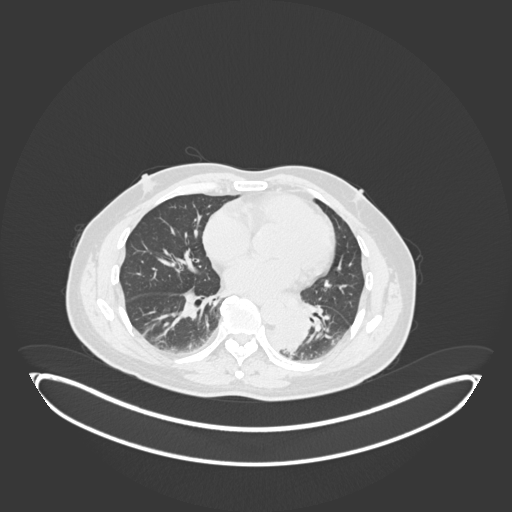
Chest CT, one axial slice; position 79 of 258 along the scan axis; lung window (W 1500 / L -600 HU); 512 × 512 image matrix, field of view 500 × 500 mm. Patient: male, 54 years. Case-level facts recorded for this patient, not image findings: clinical TNM (as recorded): T3 N0 M0.
Outlined on this slice (rectangle marked by the reading radiologist):
- lung tumour (recorded histology: squamous cell carcinoma): bounding box (x1, y1, x2, y2) in pixels: (263, 305, 308, 354)